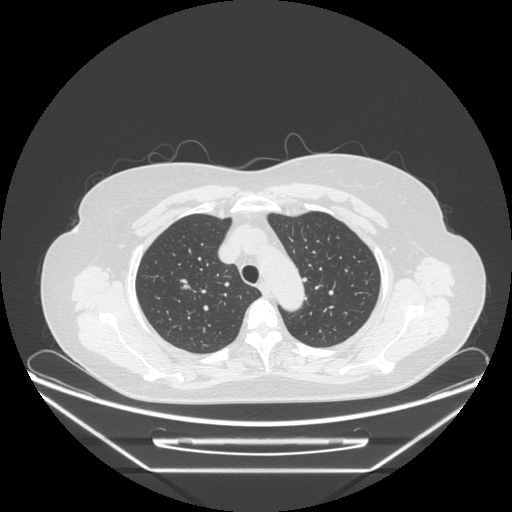
Chest CT, one axial slice; slice 191 of 236 in the series (ordered by position); reconstruction kernel STANDARD; 120 kVp; lung window (W 1500 / L -600 HU); 512 × 512 image matrix, field of view 433 × 433 mm. Patient: female, 60 years. Case-level facts recorded for this patient, not image findings: clinical TNM (as recorded): T1c N0 M0.
Annotated regions visible in this slice (bounding box drawn by a radiologist):
- lung tumour (recorded histology: adenocarcinoma): bounding box (x1, y1, x2, y2) in pixels: (171, 274, 204, 301)